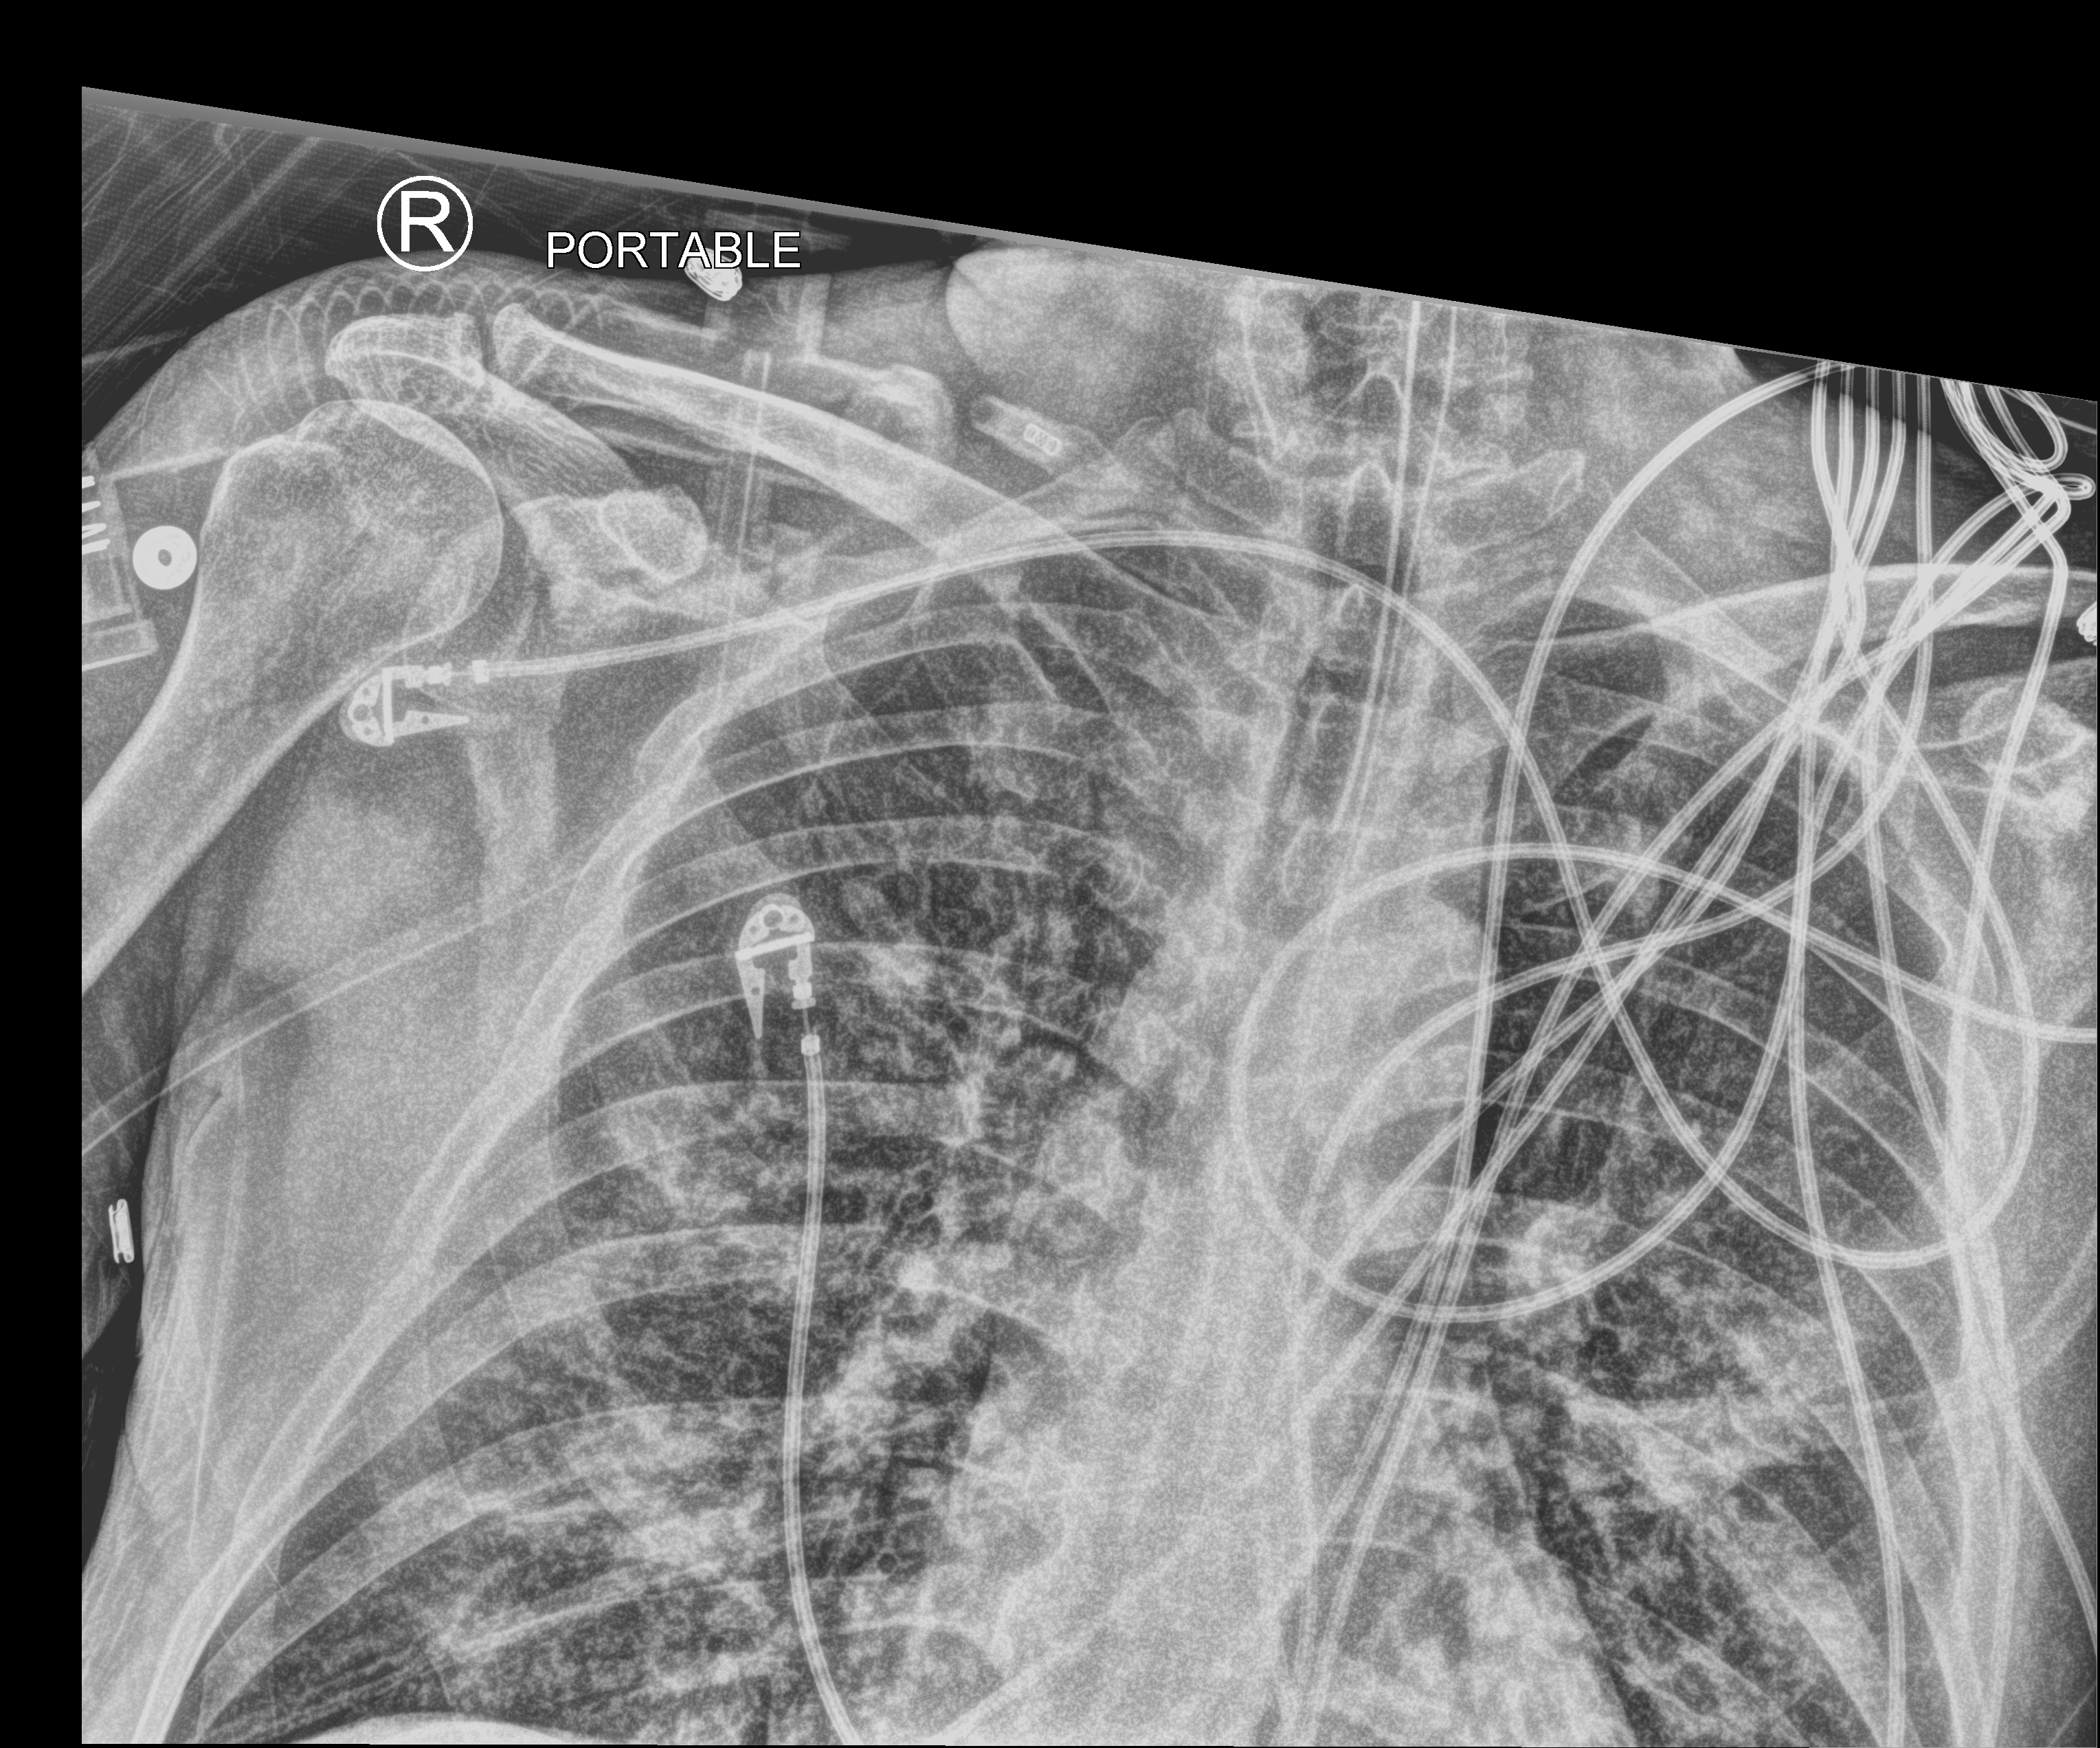
Bedside chest radiograph (computed radiography); anteroposterior (AP) projection. Male patient hospitalised with COVID-19, age 18–59 years.
From the hospital-stay record, not from the radiograph (when in the stay this image was taken is not recorded): admitted to intensive care during this hospital stay: no; chronic kidney disease (admission record): no; length of hospital stay: 19 days.